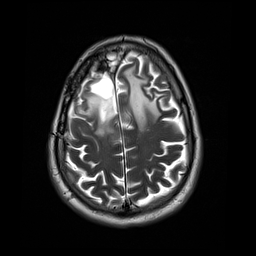
Brain MRI from a brain-tumour surgery series, one axial slice; slice 11 of 44 in the series (ordered by position); 4 mm slice thickness; 256 × 256 image matrix, field of view 240 × 240 mm. Case-level facts recorded for this patient, not image findings: histopathology: Astrocytoma; WHO grade: 4; IDH mutation: yes; tumour location: Right Frontal.
Outlined on this slice (expert manual segmentation):
- tumour: box from (x=74, y=91) to (x=116, y=138) px